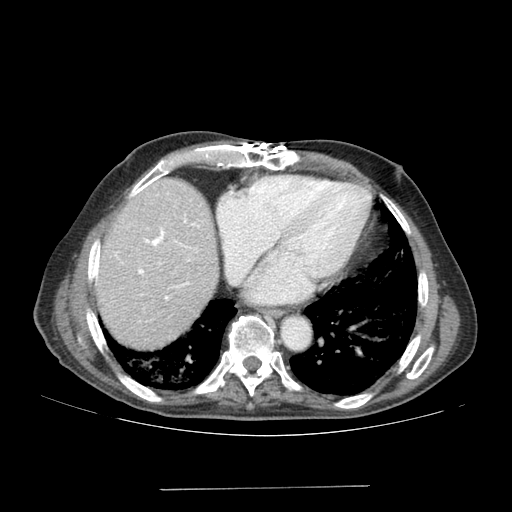
Contrast-enhanced abdominal CT (liver protocol), one axial slice; slice 156 of 192 in the series (ordered by position); soft-tissue window (W 400 / L 40 HU); 512 × 512 image matrix, field of view 400 × 400 mm. Case-level facts recorded for this patient, not image findings: diagnosis: hepatocellular carcinoma (patient treated with transarterial chemoembolisation; whether this scan precedes or follows treatment is not stated here); TNM stage (as recorded): Stage-IVA; Child-Pugh class: A; tumour differentiation: poorly differentiated; tumour nodularity: uninodular.
Outlined on this slice (semi-automatic segmentation, software-assisted and operator-edited):
- liver parenchyma outside the tumour (the mass and vessels are separate outlines, so this box may not span the whole liver): bounding box (x1, y1, x2, y2) in pixels: (94, 178, 218, 348)
- liver vessels: (131, 186, 194, 299)